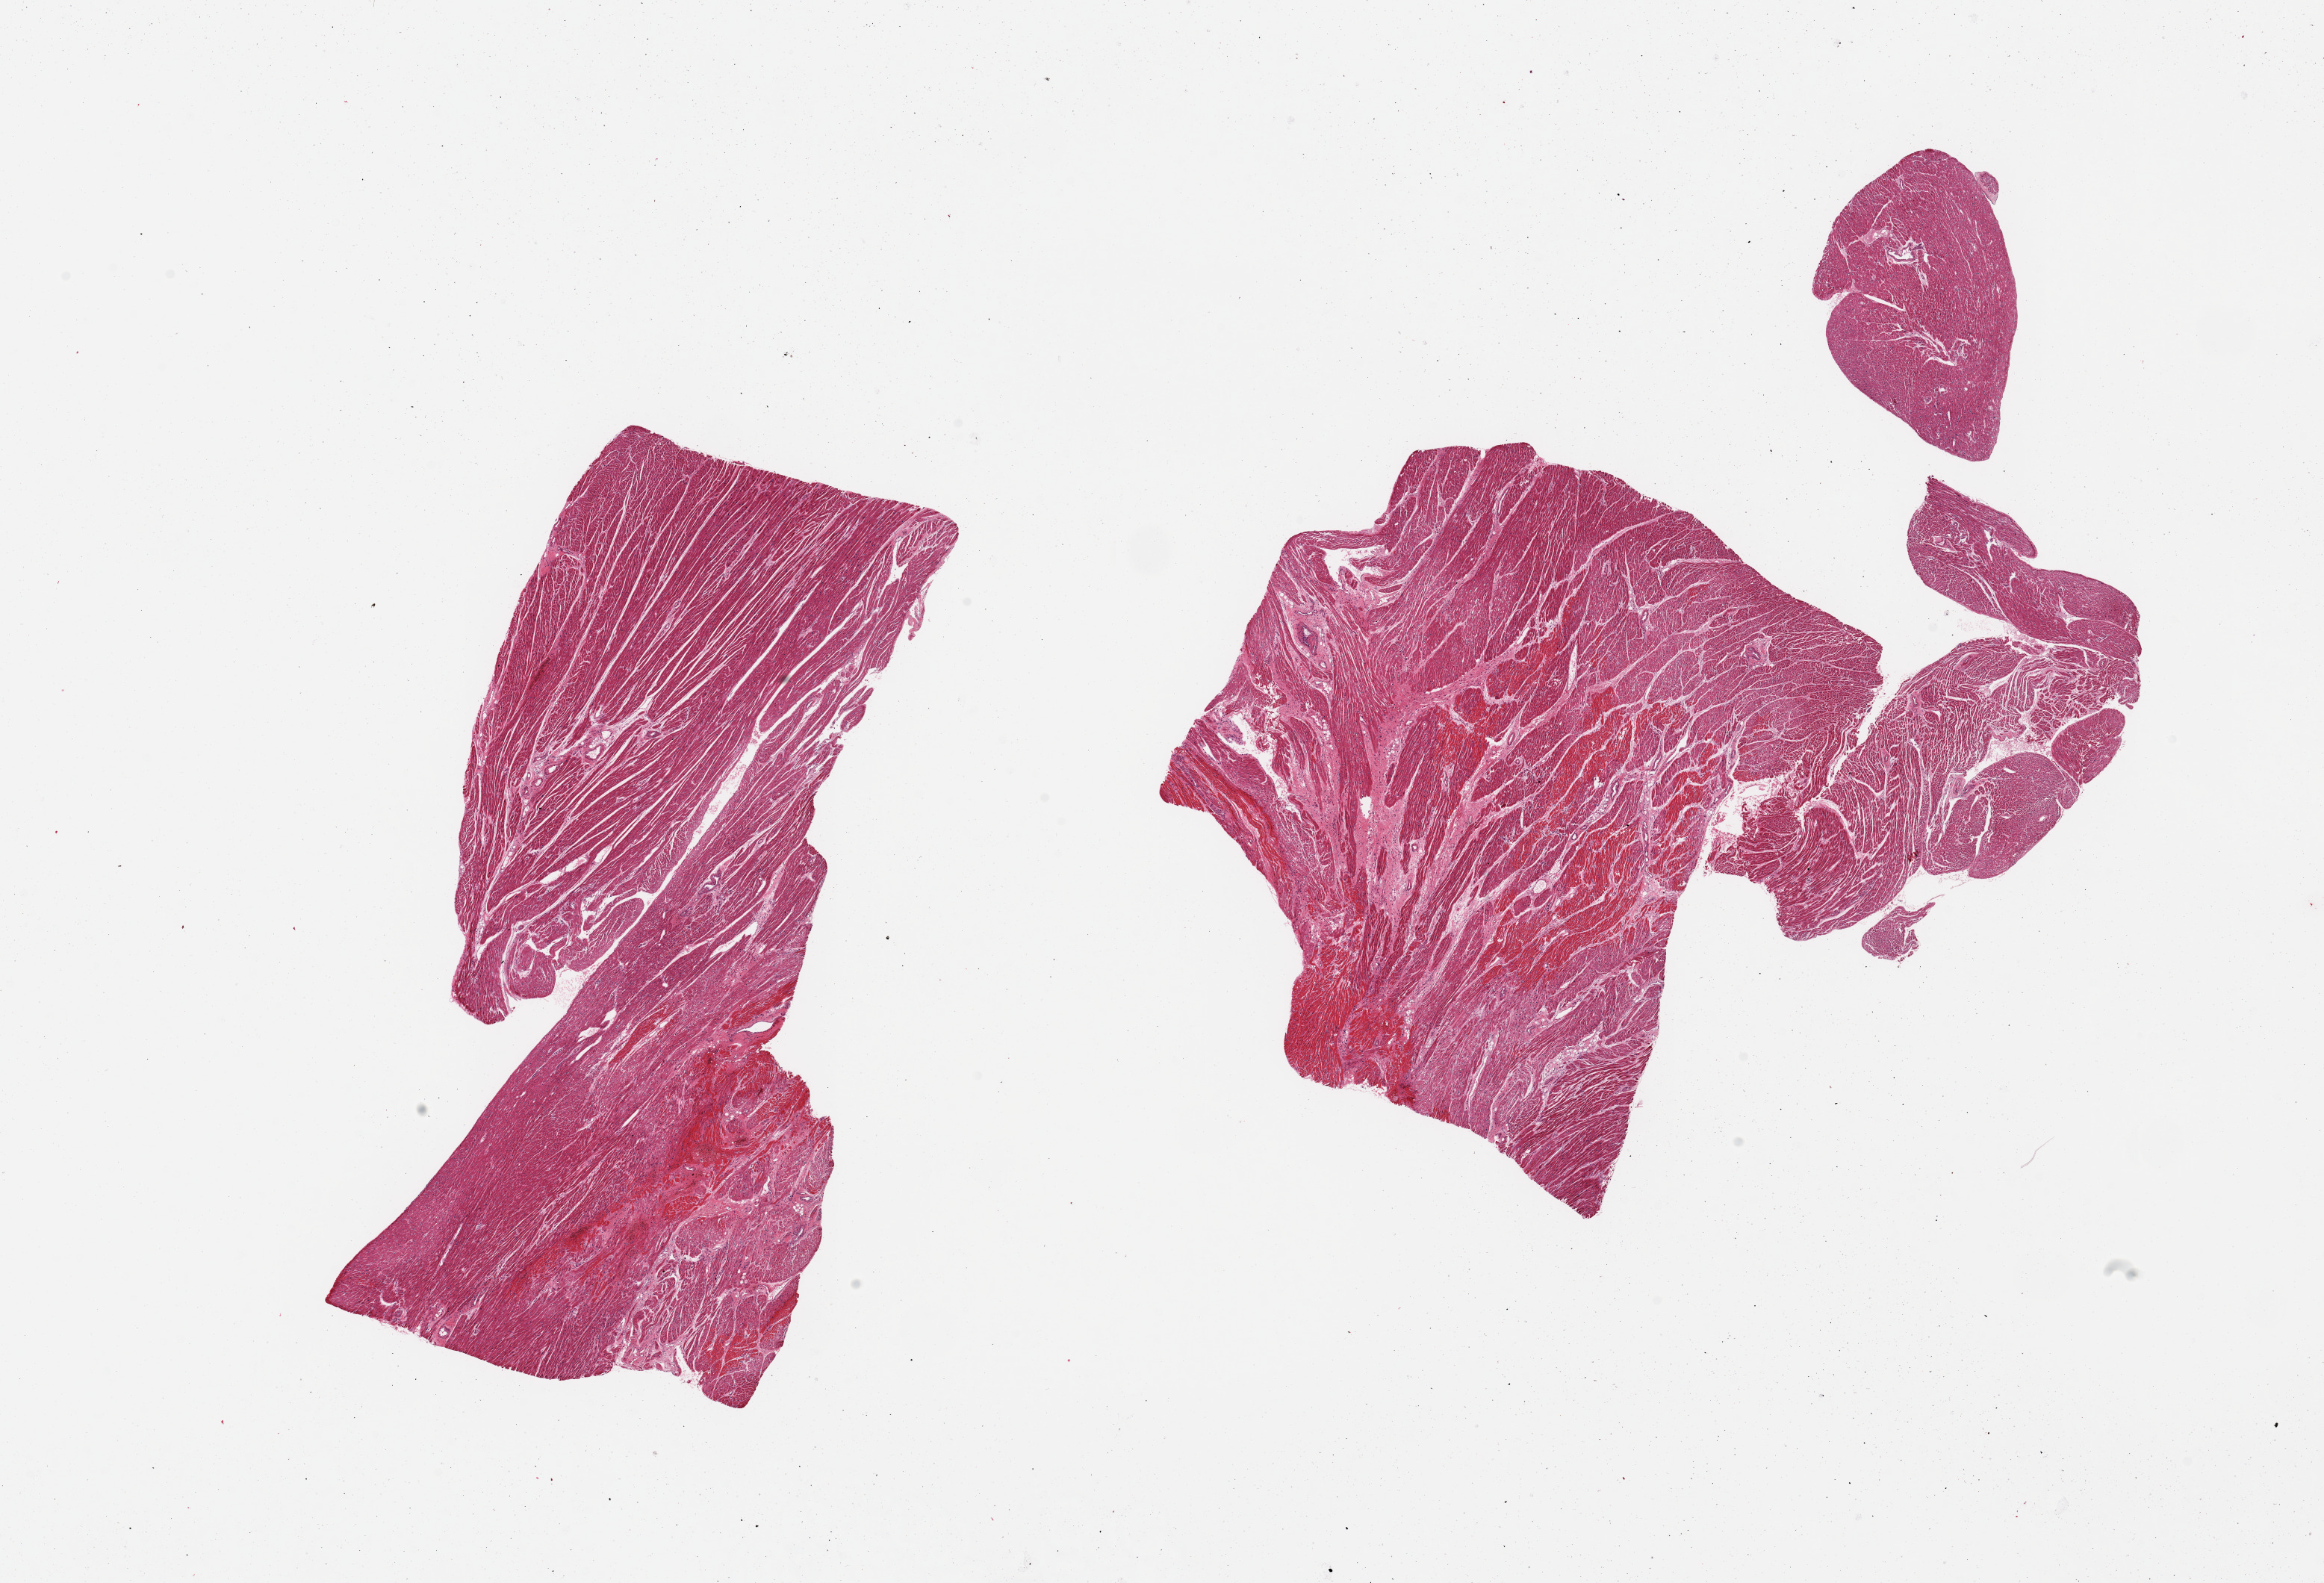
Whole-slide image, H&E stain — a low-resolution overview of the entire scanned area, about 24.6 x 16.8 mm (acquisition: 20x scan), PAXgene-fixed, paraffin-embedded tissue, target tissue: heart, tissue donor sample. Male donor.
Review note (as recorded): 2 pieces; foci of hypereosinophilia (ischemic) and fibrosis.